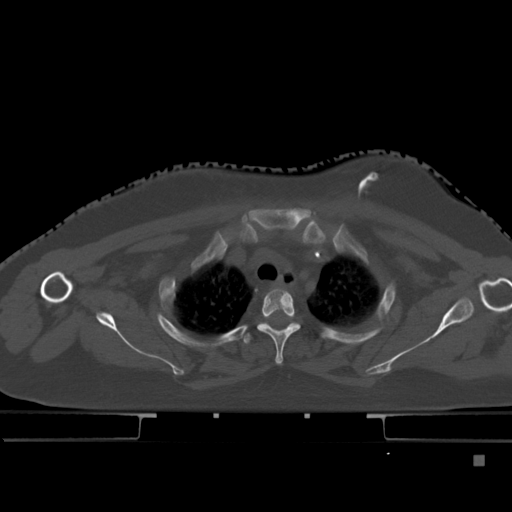
CT including the spine, one axial slice. Slice 356 of 495 in the series (ordered by position). Bone window (W 1800 / L 400 HU). 512 × 512 image matrix, field of view 404 × 404 mm. Female patient, age 33 years. Case-level facts recorded for this patient, not image findings: primary cancer: breast; vertebrae with lytic lesions (as recorded): T1.
Outlined on this slice (semi-automatic segmentation, software-assisted and operator-edited):
- T2 vertebra: bounding box (x1, y1, x2, y2) in pixels: (257, 289, 300, 365)
- T3 vertebra: (243, 322, 300, 345)